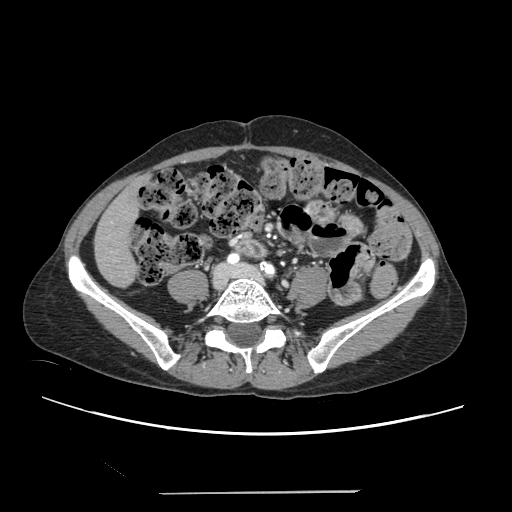
Contrast-enhanced abdominal CT, one axial slice. Slice 28 of 240 in the series (ordered by position). Intravenous contrast given. Soft-tissue window (W 400 / L 40 HU). 1.25 mm slice thickness. 512 × 512 image matrix. Female patient, age 60 years. Case-level facts recorded for this patient, not image findings: diagnosis: colorectal cancer liver metastases, imaged before liver resection; multiple liver metastases: no.
Outlined on this slice (outlined manually by an expert reader):
- liver: box from (x=96, y=181) to (x=140, y=286) px
- planned liver remnant (the part of the liver to remain after resection): (x=96, y=180)–(x=141, y=286)
- portal vein (with intrahepatic branches): (x=111, y=221)–(x=113, y=252)